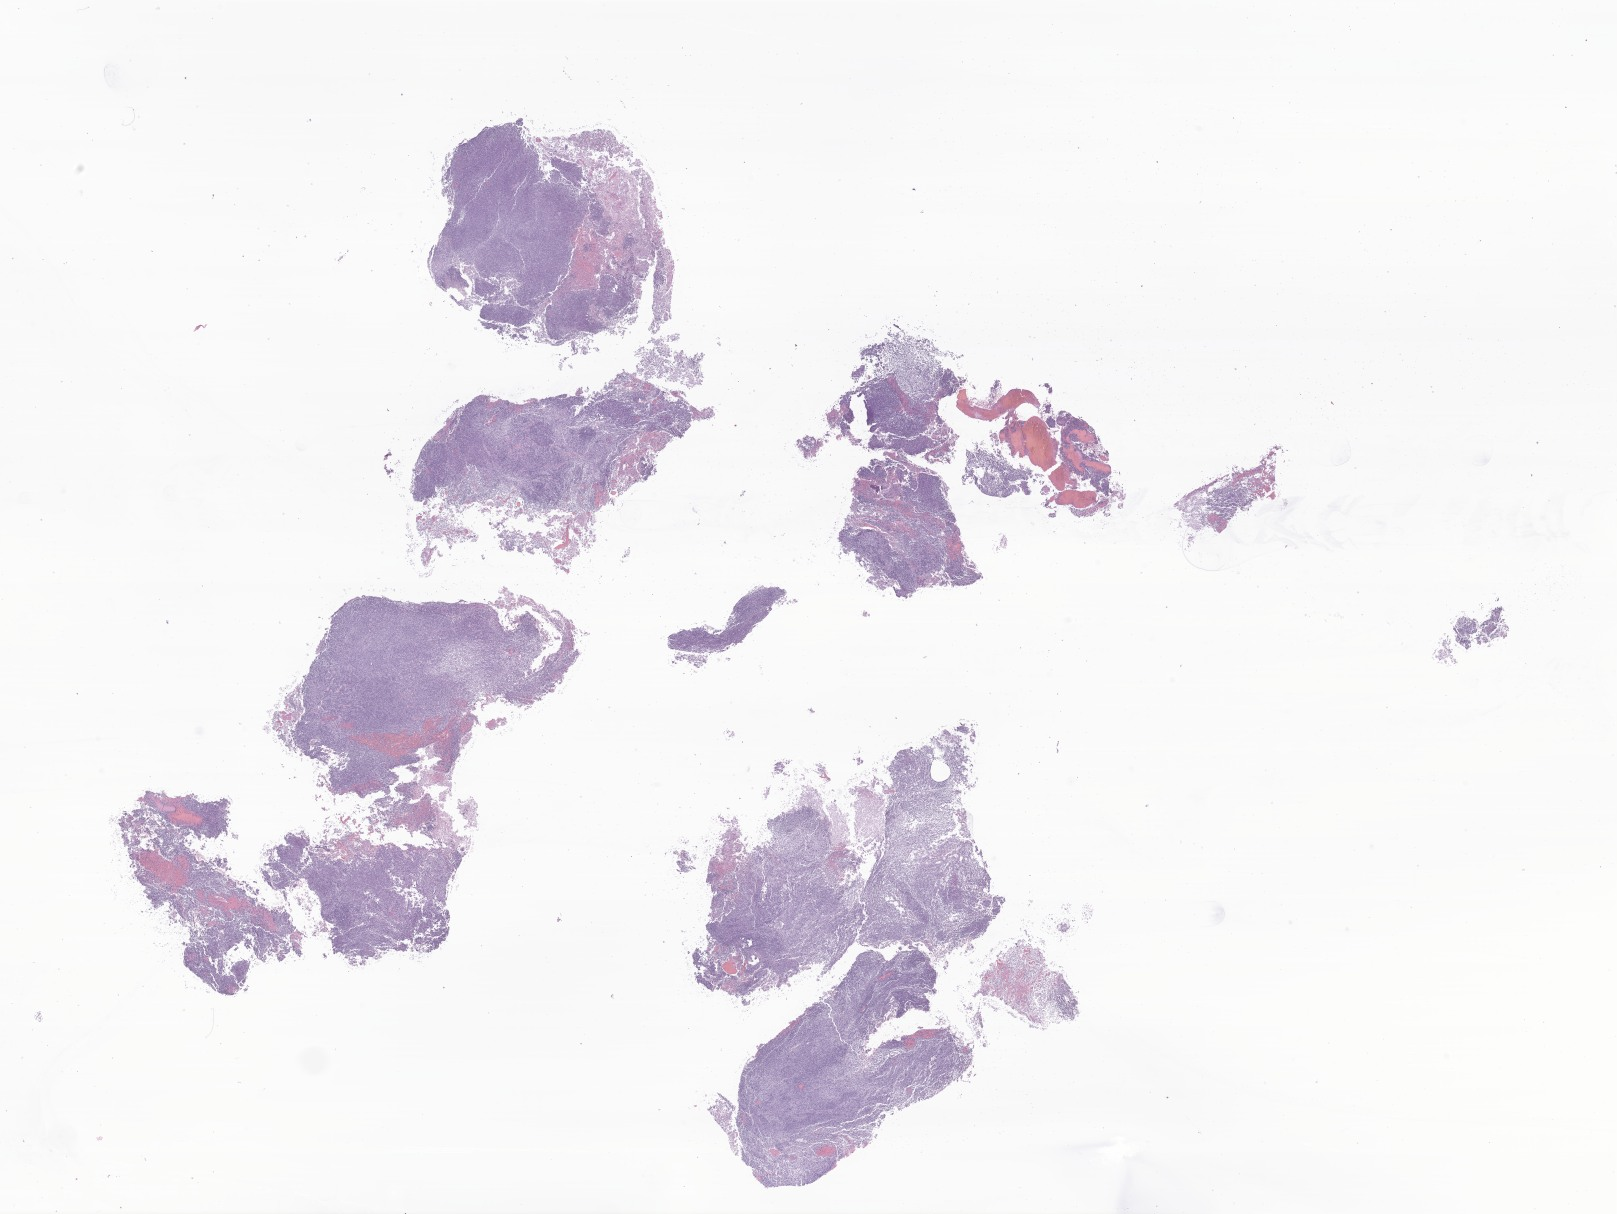
Whole-slide image, H&E stain of tumor tissue from the brain, shown as a low-resolution overview of the whole scanned area (about 27.3 x 20.5 mm); FFPE section. Patient: male, age 183 days.
Diagnosis: Neoplasm, uncertain whether benign or malignant.